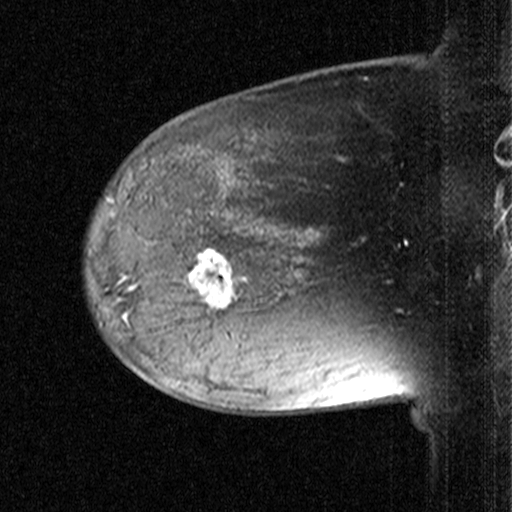
Breast MRI (dynamic contrast-enhanced), one sagittal slice; dynamic contrast-enhanced study with each time point stored as its own series, time point 2 of 3 at this slice position (early post-contrast, ordered by acquisition time); 1.5 T; TE 4.5 ms, TR 11 ms; 3 mm slice thickness; 512 × 512 image matrix. Female patient, age 38 years. From the clinical record (not read from this slice): setting: breast cancer imaged before/during neoadjuvant chemotherapy; receptor status: HR-positive, HER2-negative.
Annotated regions visible in this slice (semi-automatic segmentation, software-assisted and operator-edited):
- analysis volume of interest (the breast-tissue region the enhancement analysis was run in; not a lesion): bounding box <170,232,259,331> (left, top, right, bottom; pixels)
- tumour enhancement mask (voxels above the 90 % enhancement threshold inside the analysis volume of interest): <192,249,239,308>